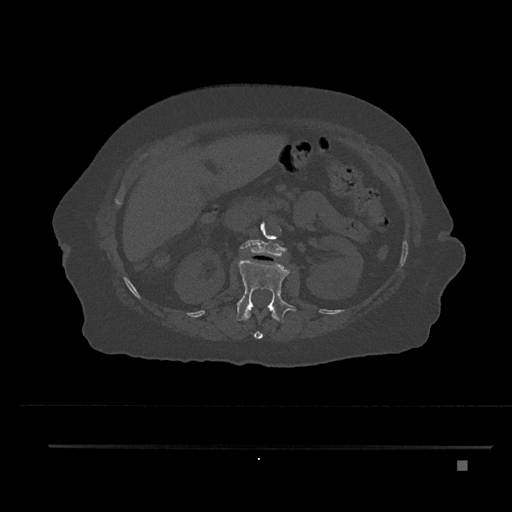
CT including the spine, one axial slice; position 222 of 797 along the scan axis; 120 kVp; bone window (W 1800 / L 400 HU); 0.5 mm slice thickness; 512 × 512 image matrix. Patient: female, 76 years. Case-level facts recorded for this patient, not image findings: primary cancer: lung.
Outlined on this slice (semi-automatic segmentation, software-assisted and operator-edited):
- L1 vertebra: box from (x=236, y=259) to (x=296, y=324) px
- L2 vertebra: (x=241, y=239)–(x=286, y=256)
- T12 vertebra: (x=245, y=310)–(x=277, y=339)